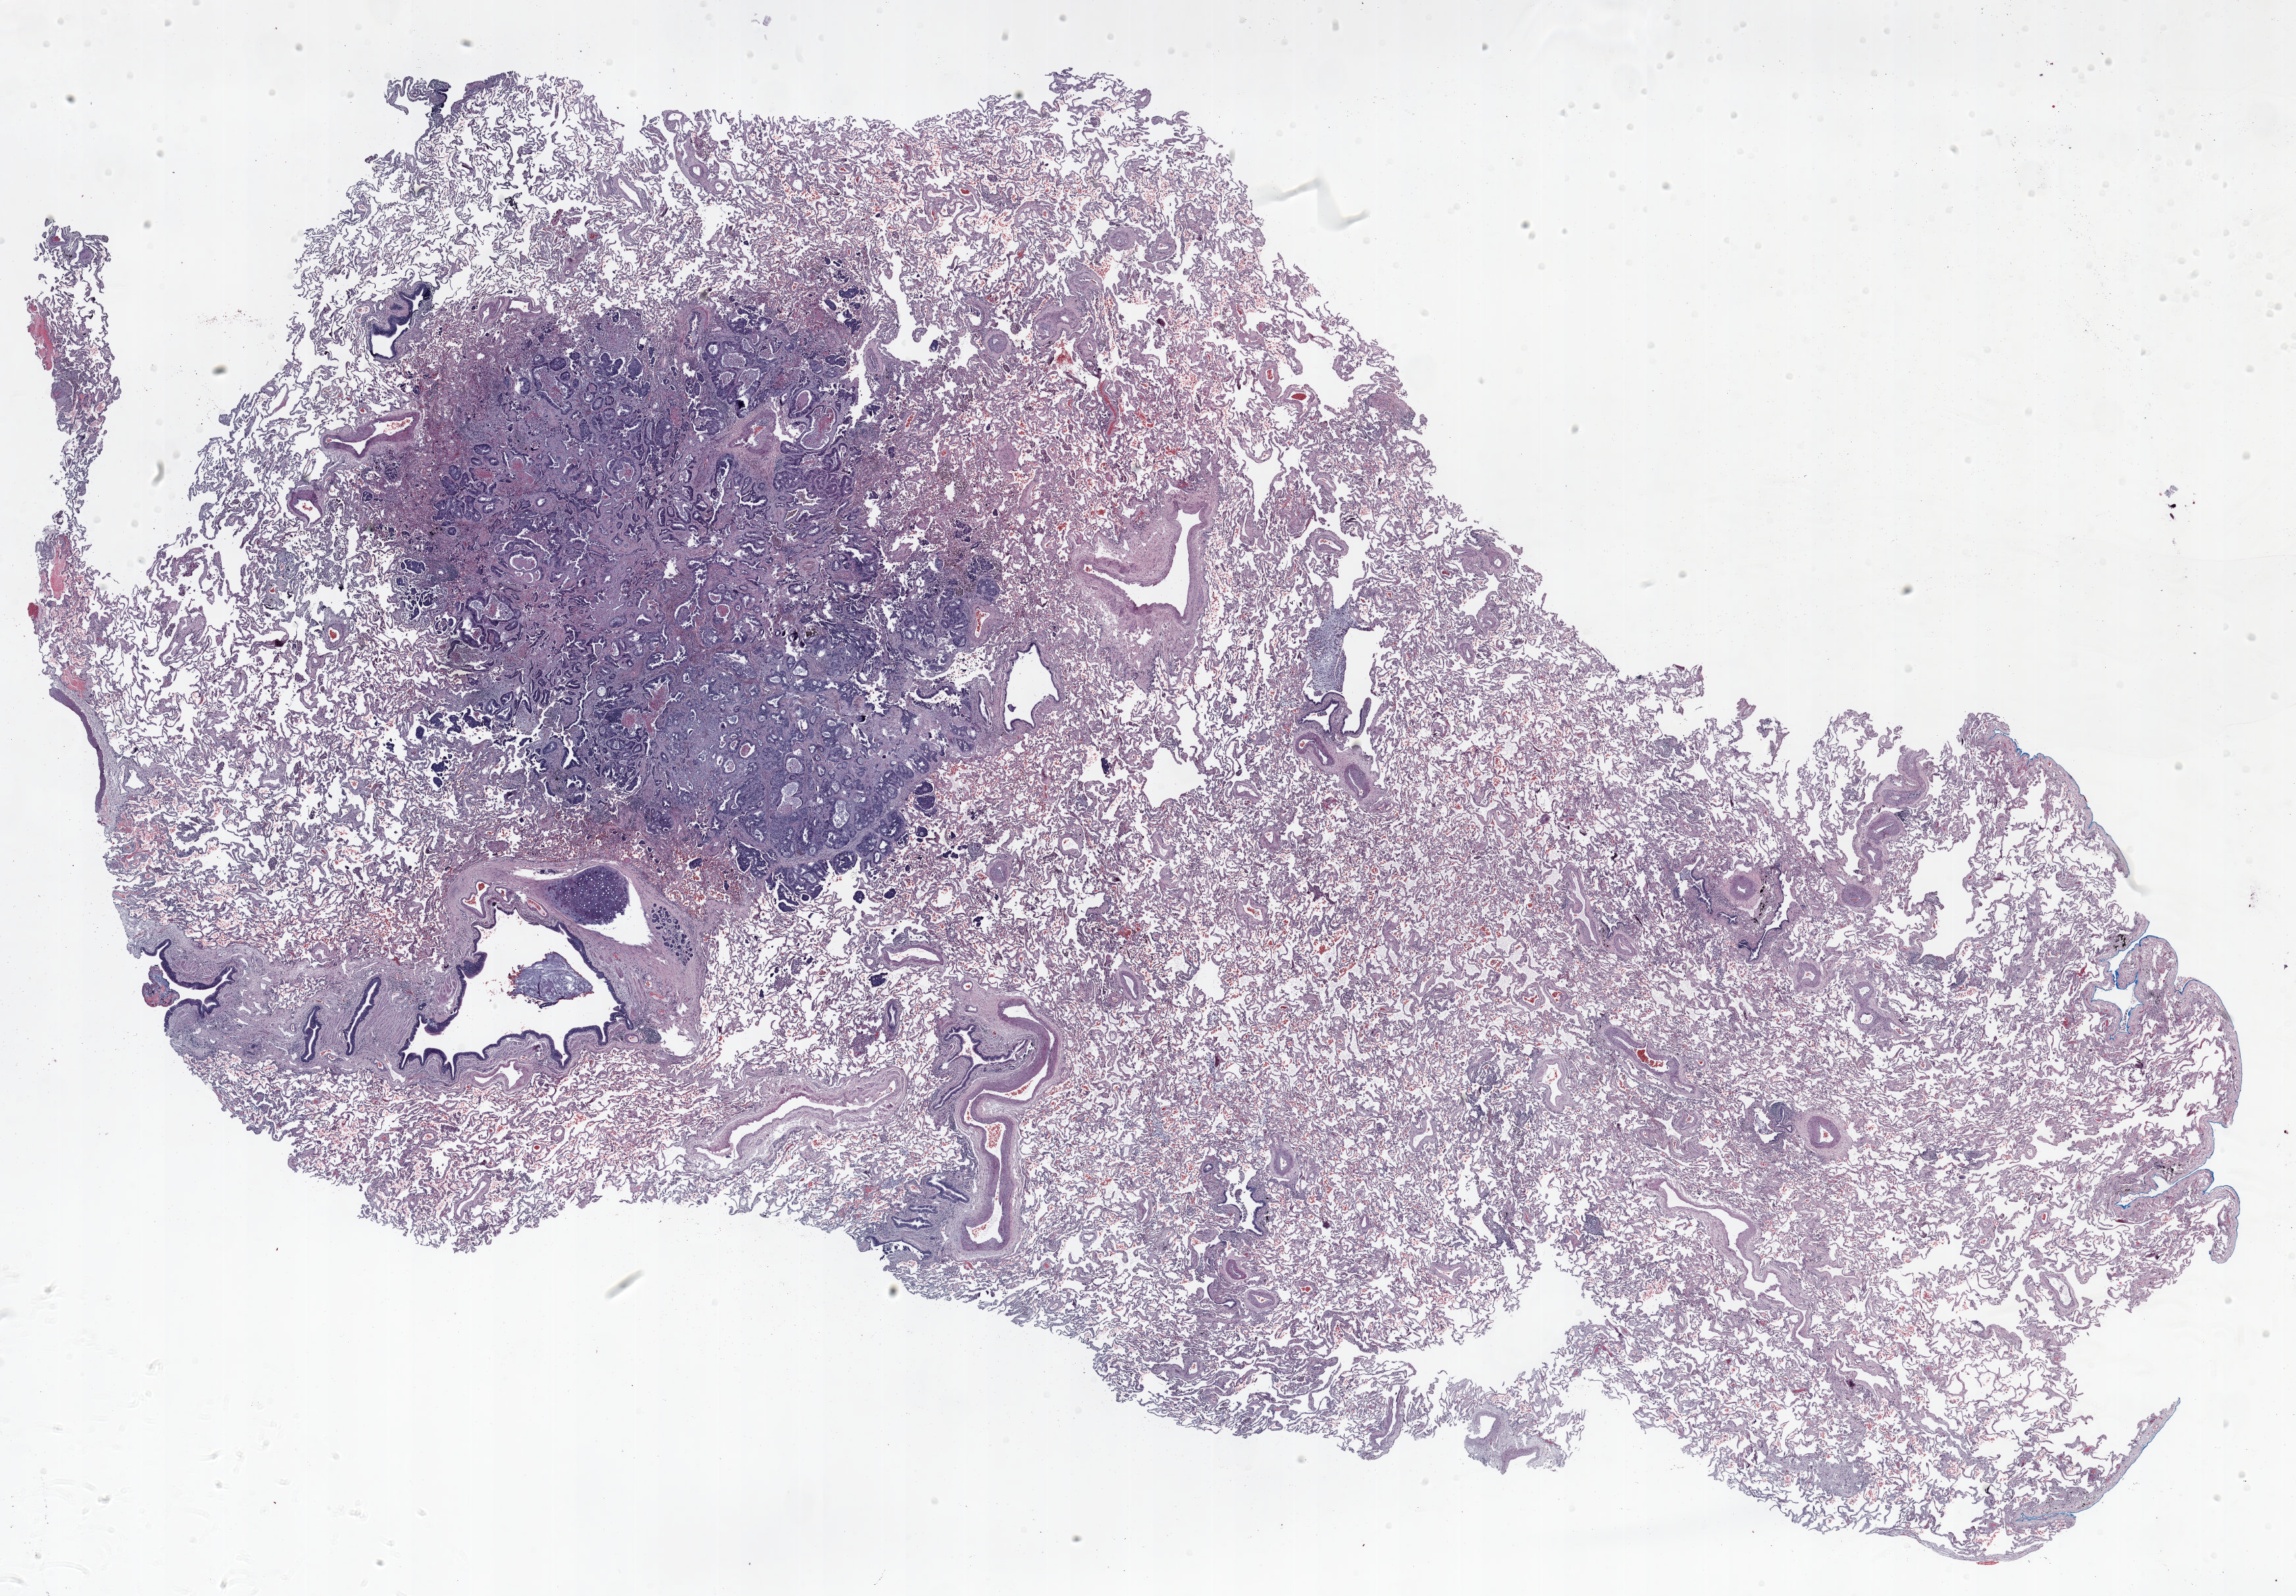
H&E whole-slide image — shown as a low-resolution overview of the whole scanned area (about 28.0 x 19.5 mm, from a 20x scan), FFPE section, lung tissue. Male patient, aged 68 at enrolment. Grade: moderately differentiated (G2).
- primary tumour location (clinical record): right upper lobe
- stage (AJCC 6th edition): IA
- tumour size (pathology): 13 mm
- participant's lung-cancer diagnosis: Adenocarcinoma, NOS